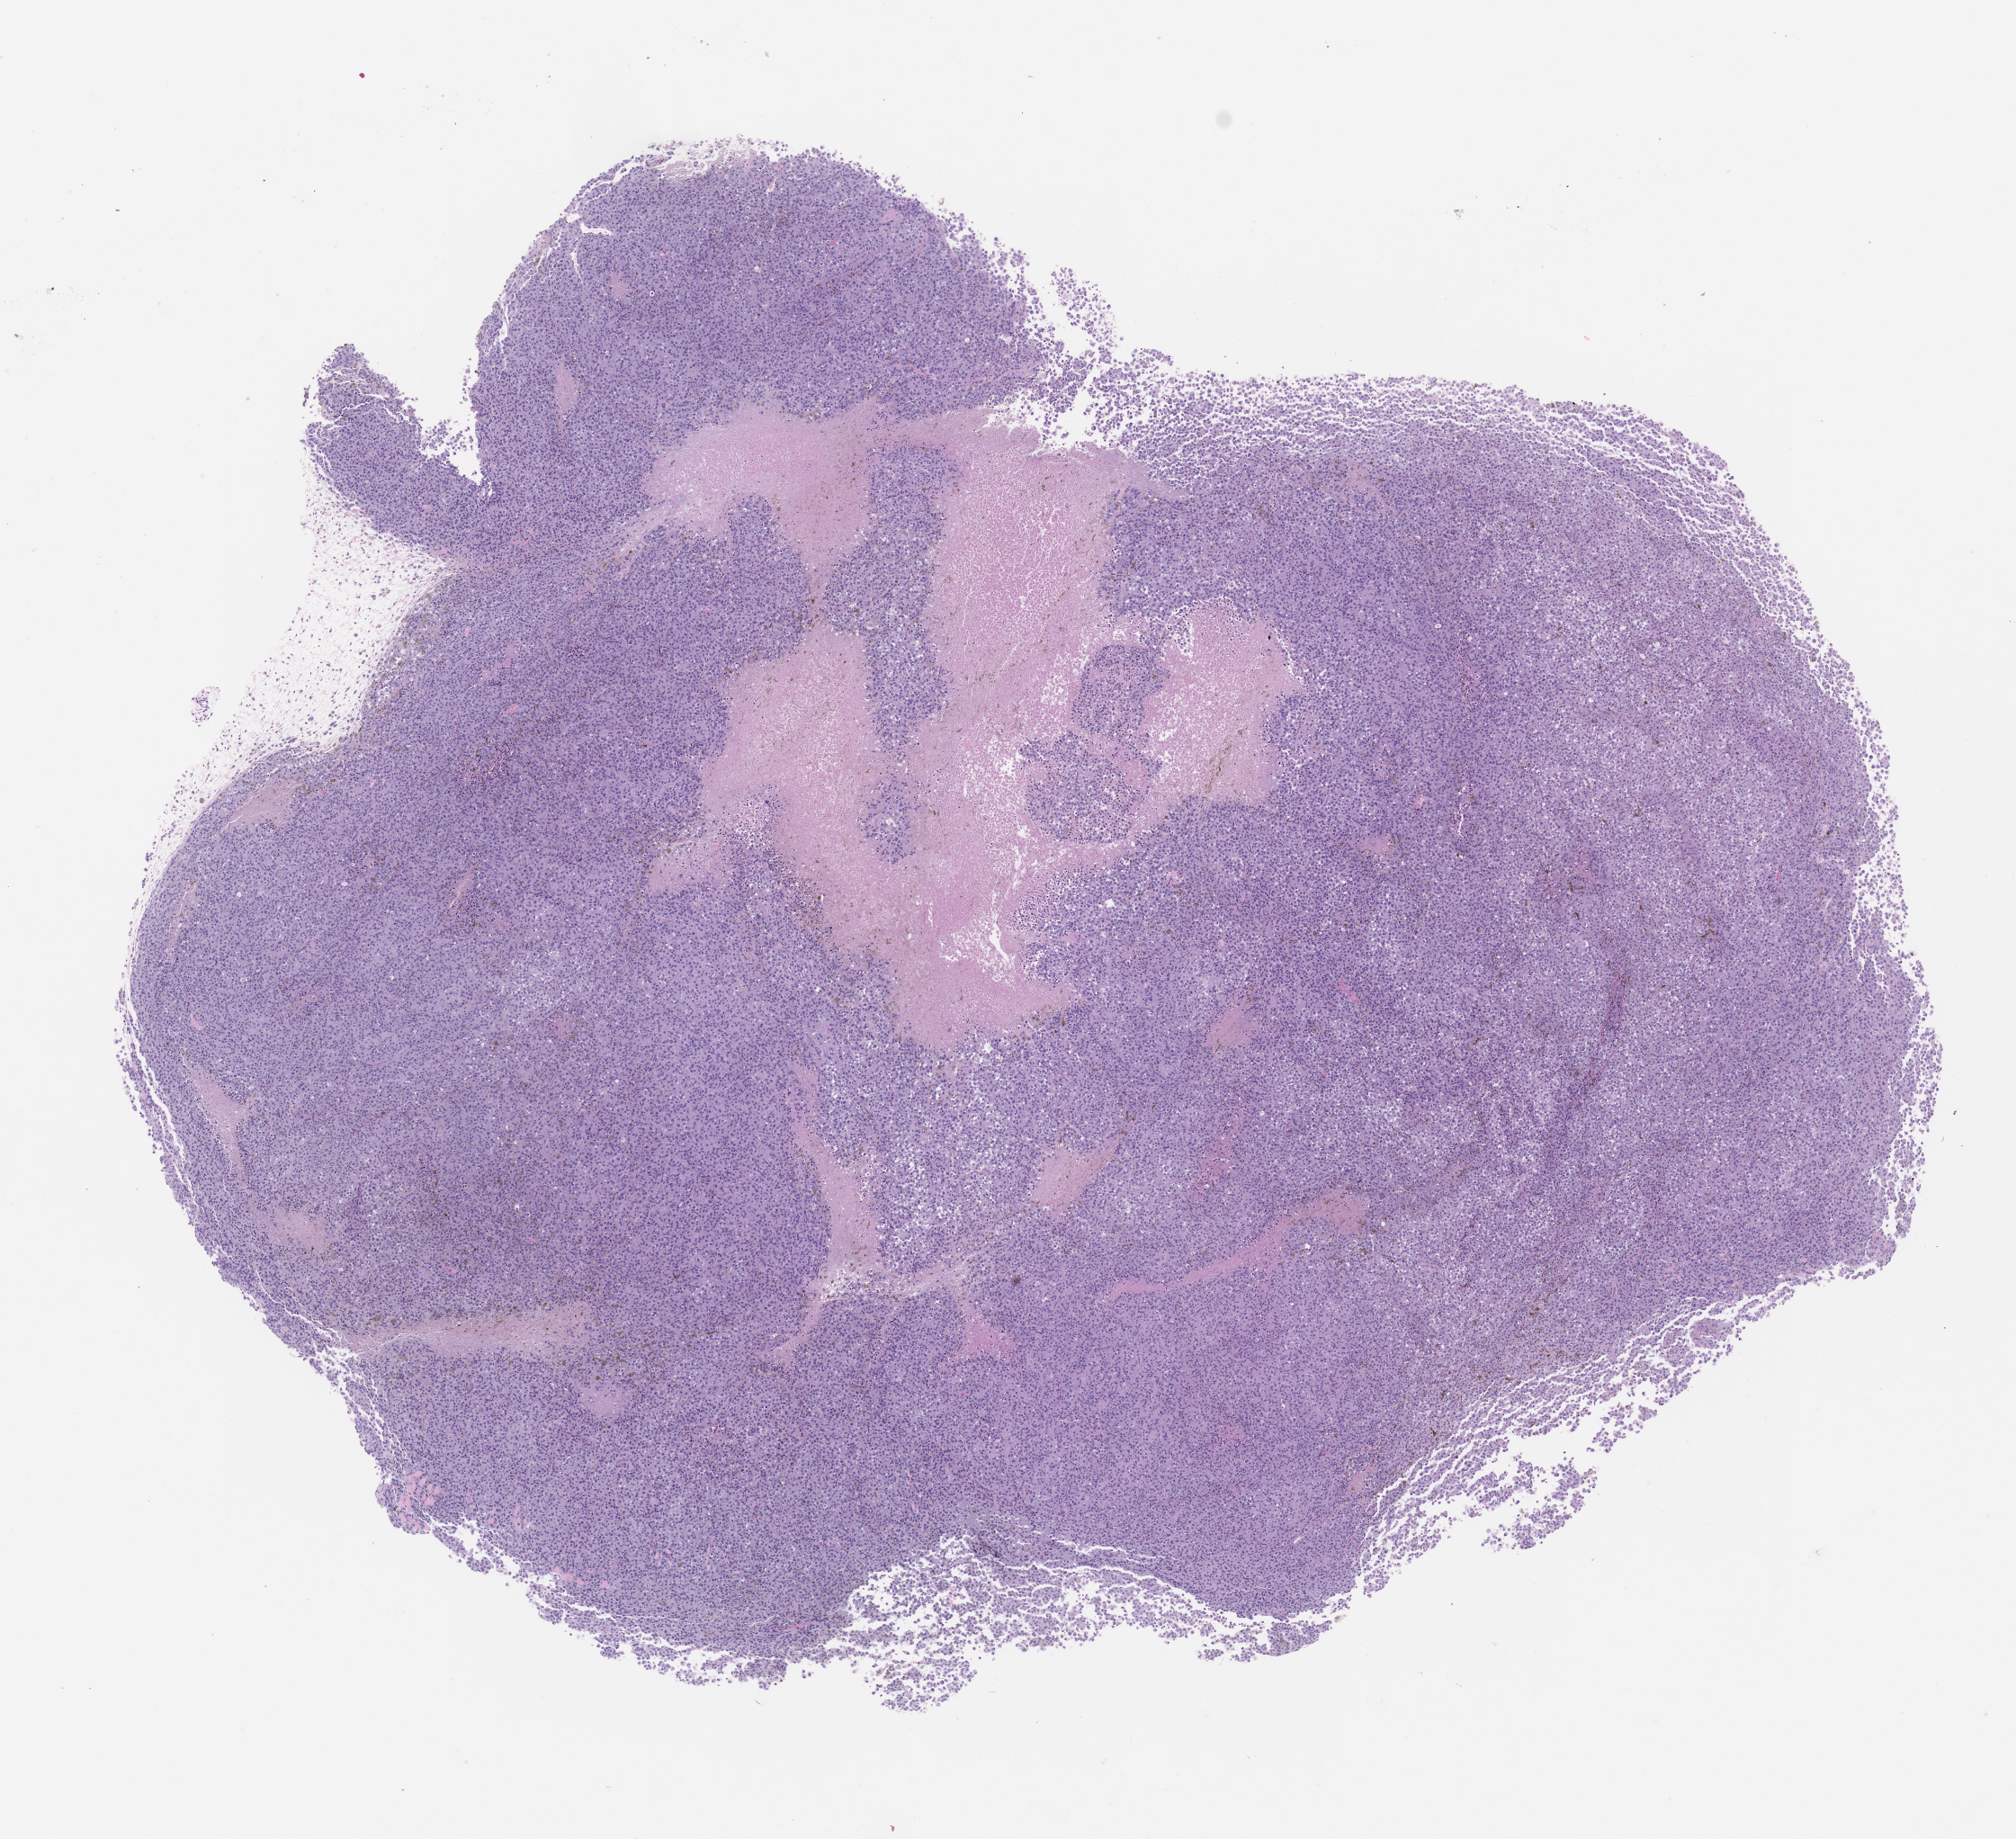
Whole-slide image, haematoxylin and eosin: patient-derived xenograft (human tumor grown in a mouse), passage 1 — shown as a low-resolution overview of the whole scanned area (about 9.0 x 8.2 mm). FFPE section. Tumor site category: skin.
Originating patient diagnosis: Melanoma.